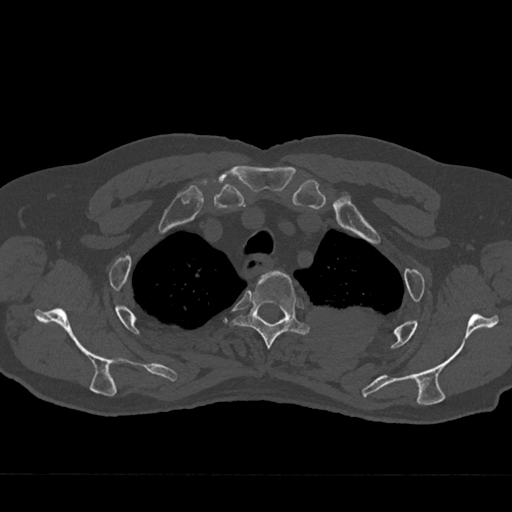
CT including the spine, one axial slice; slice 571 of 797 in the series (ordered by position); 120 kVp; bone window (W 1800 / L 400 HU); 0.5 mm slice thickness; 512 × 512 image matrix, field of view 377 × 377 mm. Patient: male, 75 years. Case-level facts recorded for this patient, not image findings: primary cancer: renal; vertebrae with lytic lesions (as recorded): T4.
Structures marked on this image (semi-automatic segmentation, software-assisted and operator-edited):
- T3 vertebra: bounding box (x1, y1, x2, y2) in pixels: (232, 270, 310, 349)